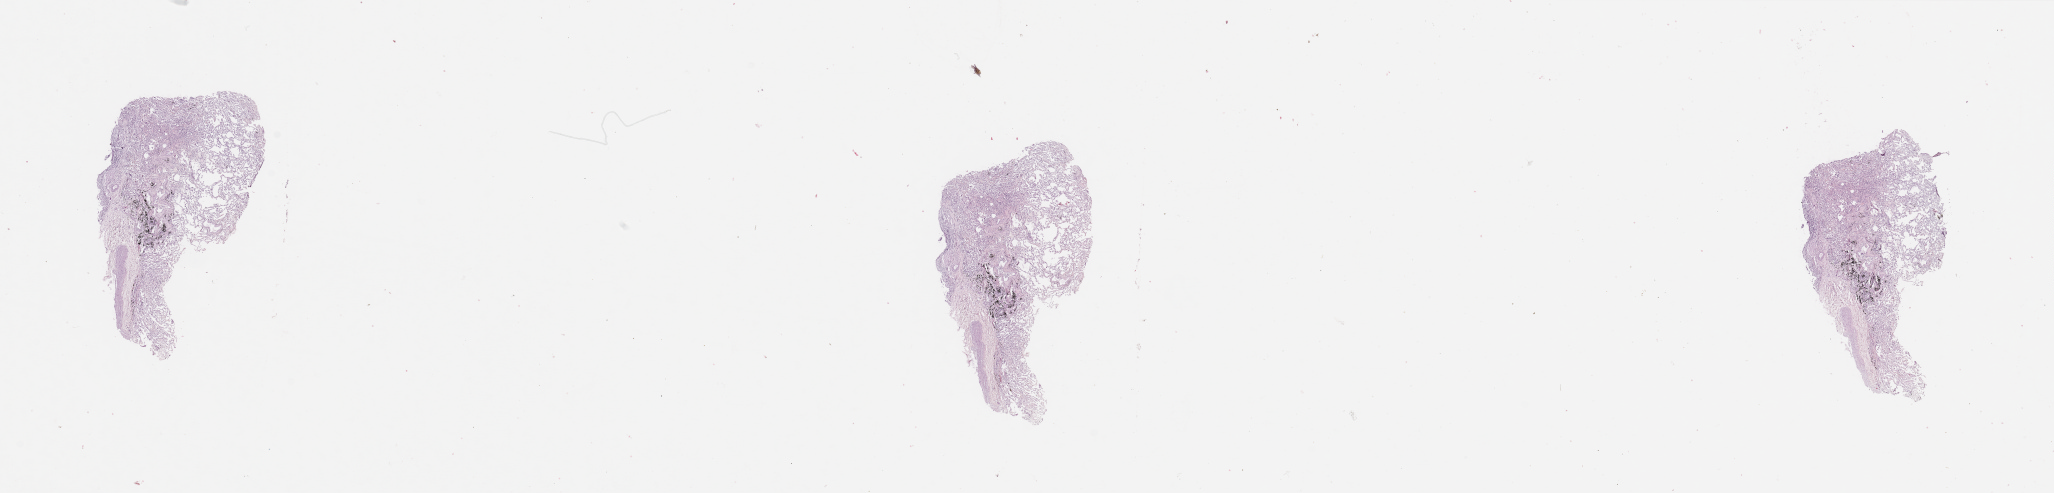
Hematoxylin and eosin (H&E) stained whole-slide image — a low-resolution overview of the entire scanned area, about 32.5 x 7.8 mm; normal (non-tumour) tissue sample, lung. Male, 77 y/o.
This section: normal (non-tumour) tissue from the same patient. Patient diagnosis: Adenocarcinoma, NOS.